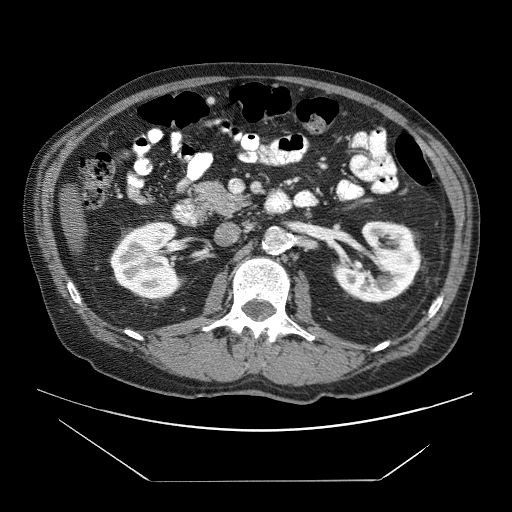
Contrast-enhanced abdominal CT (liver protocol), one axial slice. Slice 10 of 83 in the series (ordered by position). Reconstruction kernel STANDARD. Soft-tissue window (W 400 / L 40 HU). 2.5 mm slice thickness. 512 × 512 image matrix, field of view 420 × 420 mm. Case-level facts recorded for this patient, not image findings: diagnosis: hepatocellular carcinoma (patient treated with transarterial chemoembolisation; whether this scan precedes or follows treatment is not stated here); TNM stage (as recorded): Stage-IVB.
Annotated regions visible in this slice (semi-automatic segmentation, software-assisted and operator-edited):
- liver parenchyma outside the tumour (the mass and vessels are separate outlines, so this box may not span the whole liver): bounding box [x1, y1, x2, y2] px = [60, 190, 86, 252]